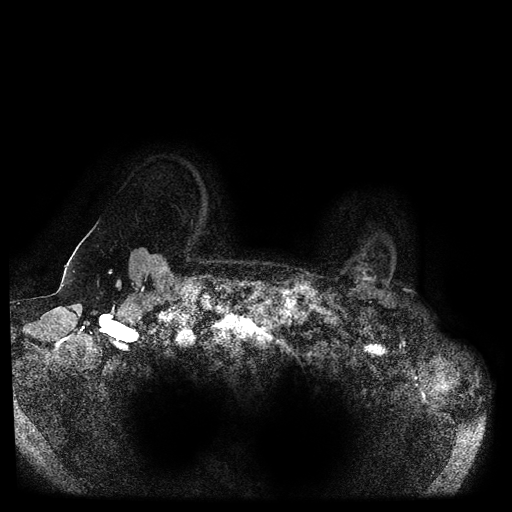
Breast MRI (dynamic contrast-enhanced, multi-phase), one axial slice. Position 91 of 116 along the scan axis. Dynamic contrast-enhanced series, time point 2 of 5 at this slice position (early post-contrast). 1.5 T. TE 2.6 ms, TR 5.3 ms. 2 mm slice thickness. 512 × 512 image matrix, field of view 370 × 370 mm. Patient: female, 55 years.
Outlined on this slice (semi-automatically segmented with operator editing):
- breast lesion (labelled benign in the annotation): bounding box <352,261,376,287> (left, top, right, bottom; pixels)